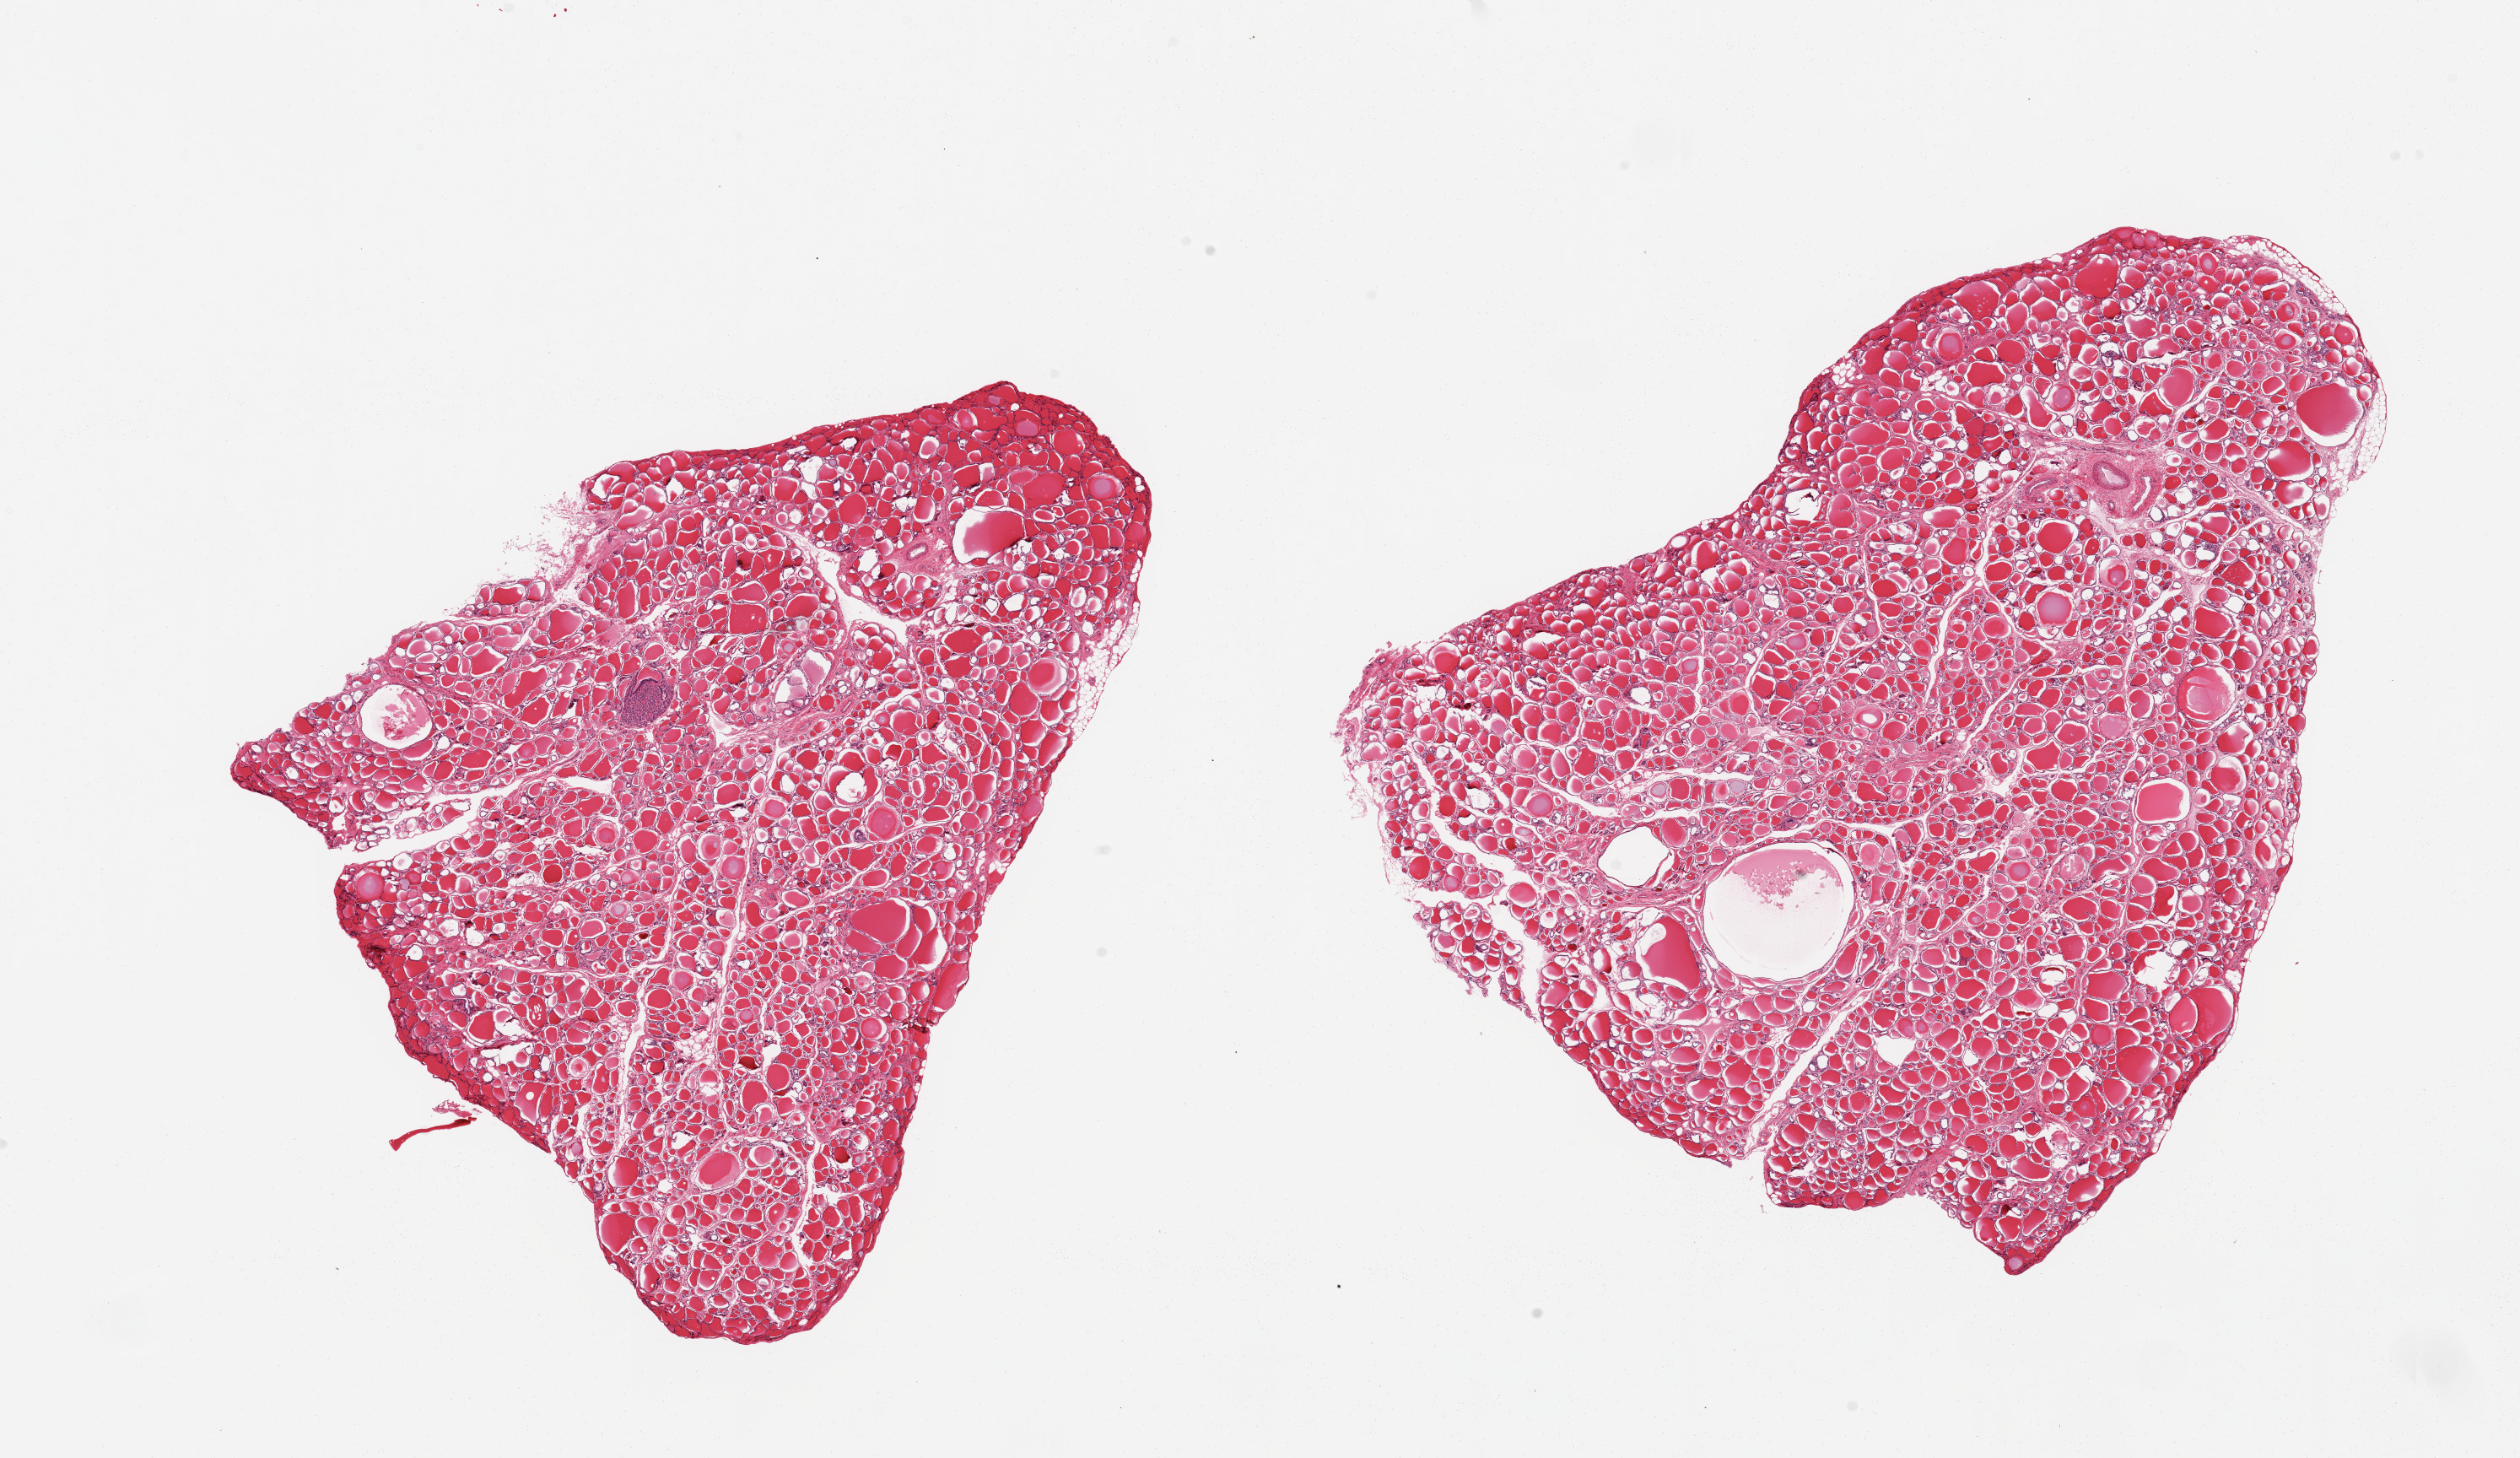
Whole-slide image, haematoxylin and eosin stain, low-resolution overview of the scanned area, about 23.6 x 13.7 mm (slide scanned at 20x). PAXgene-fixed, paraffin-embedded tissue. Section of thyroid (target tissue). Donor tissue sample. Donor sex: female.
• pathologist's review note for this sample: 2 pieces; 0.59mm adenomatoid nodule